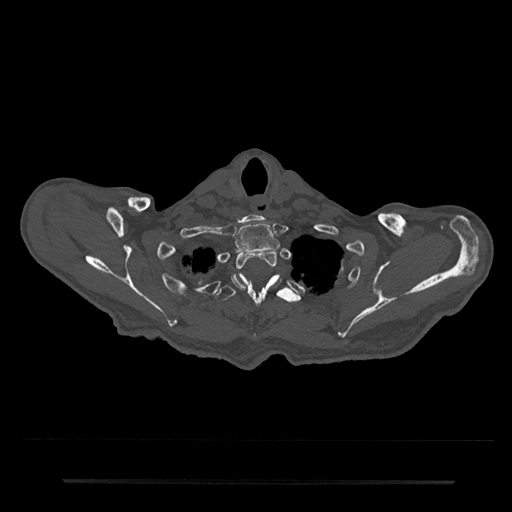
CT including the spine, one axial slice; slice 687 of 797 in the series (ordered by position); reconstruction kernel Br40s/3; 120 kVp; bone window (W 1800 / L 400 HU); 512 × 512 image matrix, field of view 427 × 427 mm. Patient: male, 74 years. Case-level facts recorded for this patient, not image findings: primary cancer: prostate.
Structures marked on this image (semi-automatic segmentation, software-assisted and operator-edited):
- T1 vertebra: bounding box (x1, y1, x2, y2) in pixels: (234, 223, 280, 253)
- T2 vertebra: (231, 250, 279, 290)
- T3 vertebra: (215, 273, 300, 340)